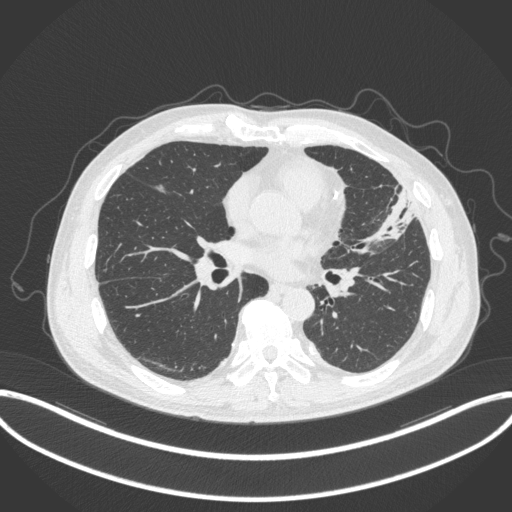
Chest CT, one axial slice; slice 158 of 382 in the series (ordered by position); reconstruction kernel B31f; 120 kVp; lung window (W 1500 / L -600 HU); 1 mm slice thickness; 512 × 512 image matrix, field of view 415 × 415 mm. Patient: male, 64 years. Case-level facts recorded for this patient, not image findings: clinical TNM (as recorded): T4 N1 M0.
Outlined on this slice (bounding box drawn by a radiologist):
- lung tumour (recorded histology: adenocarcinoma): bounding box (x1, y1, x2, y2) in pixels: (362, 188, 424, 250)